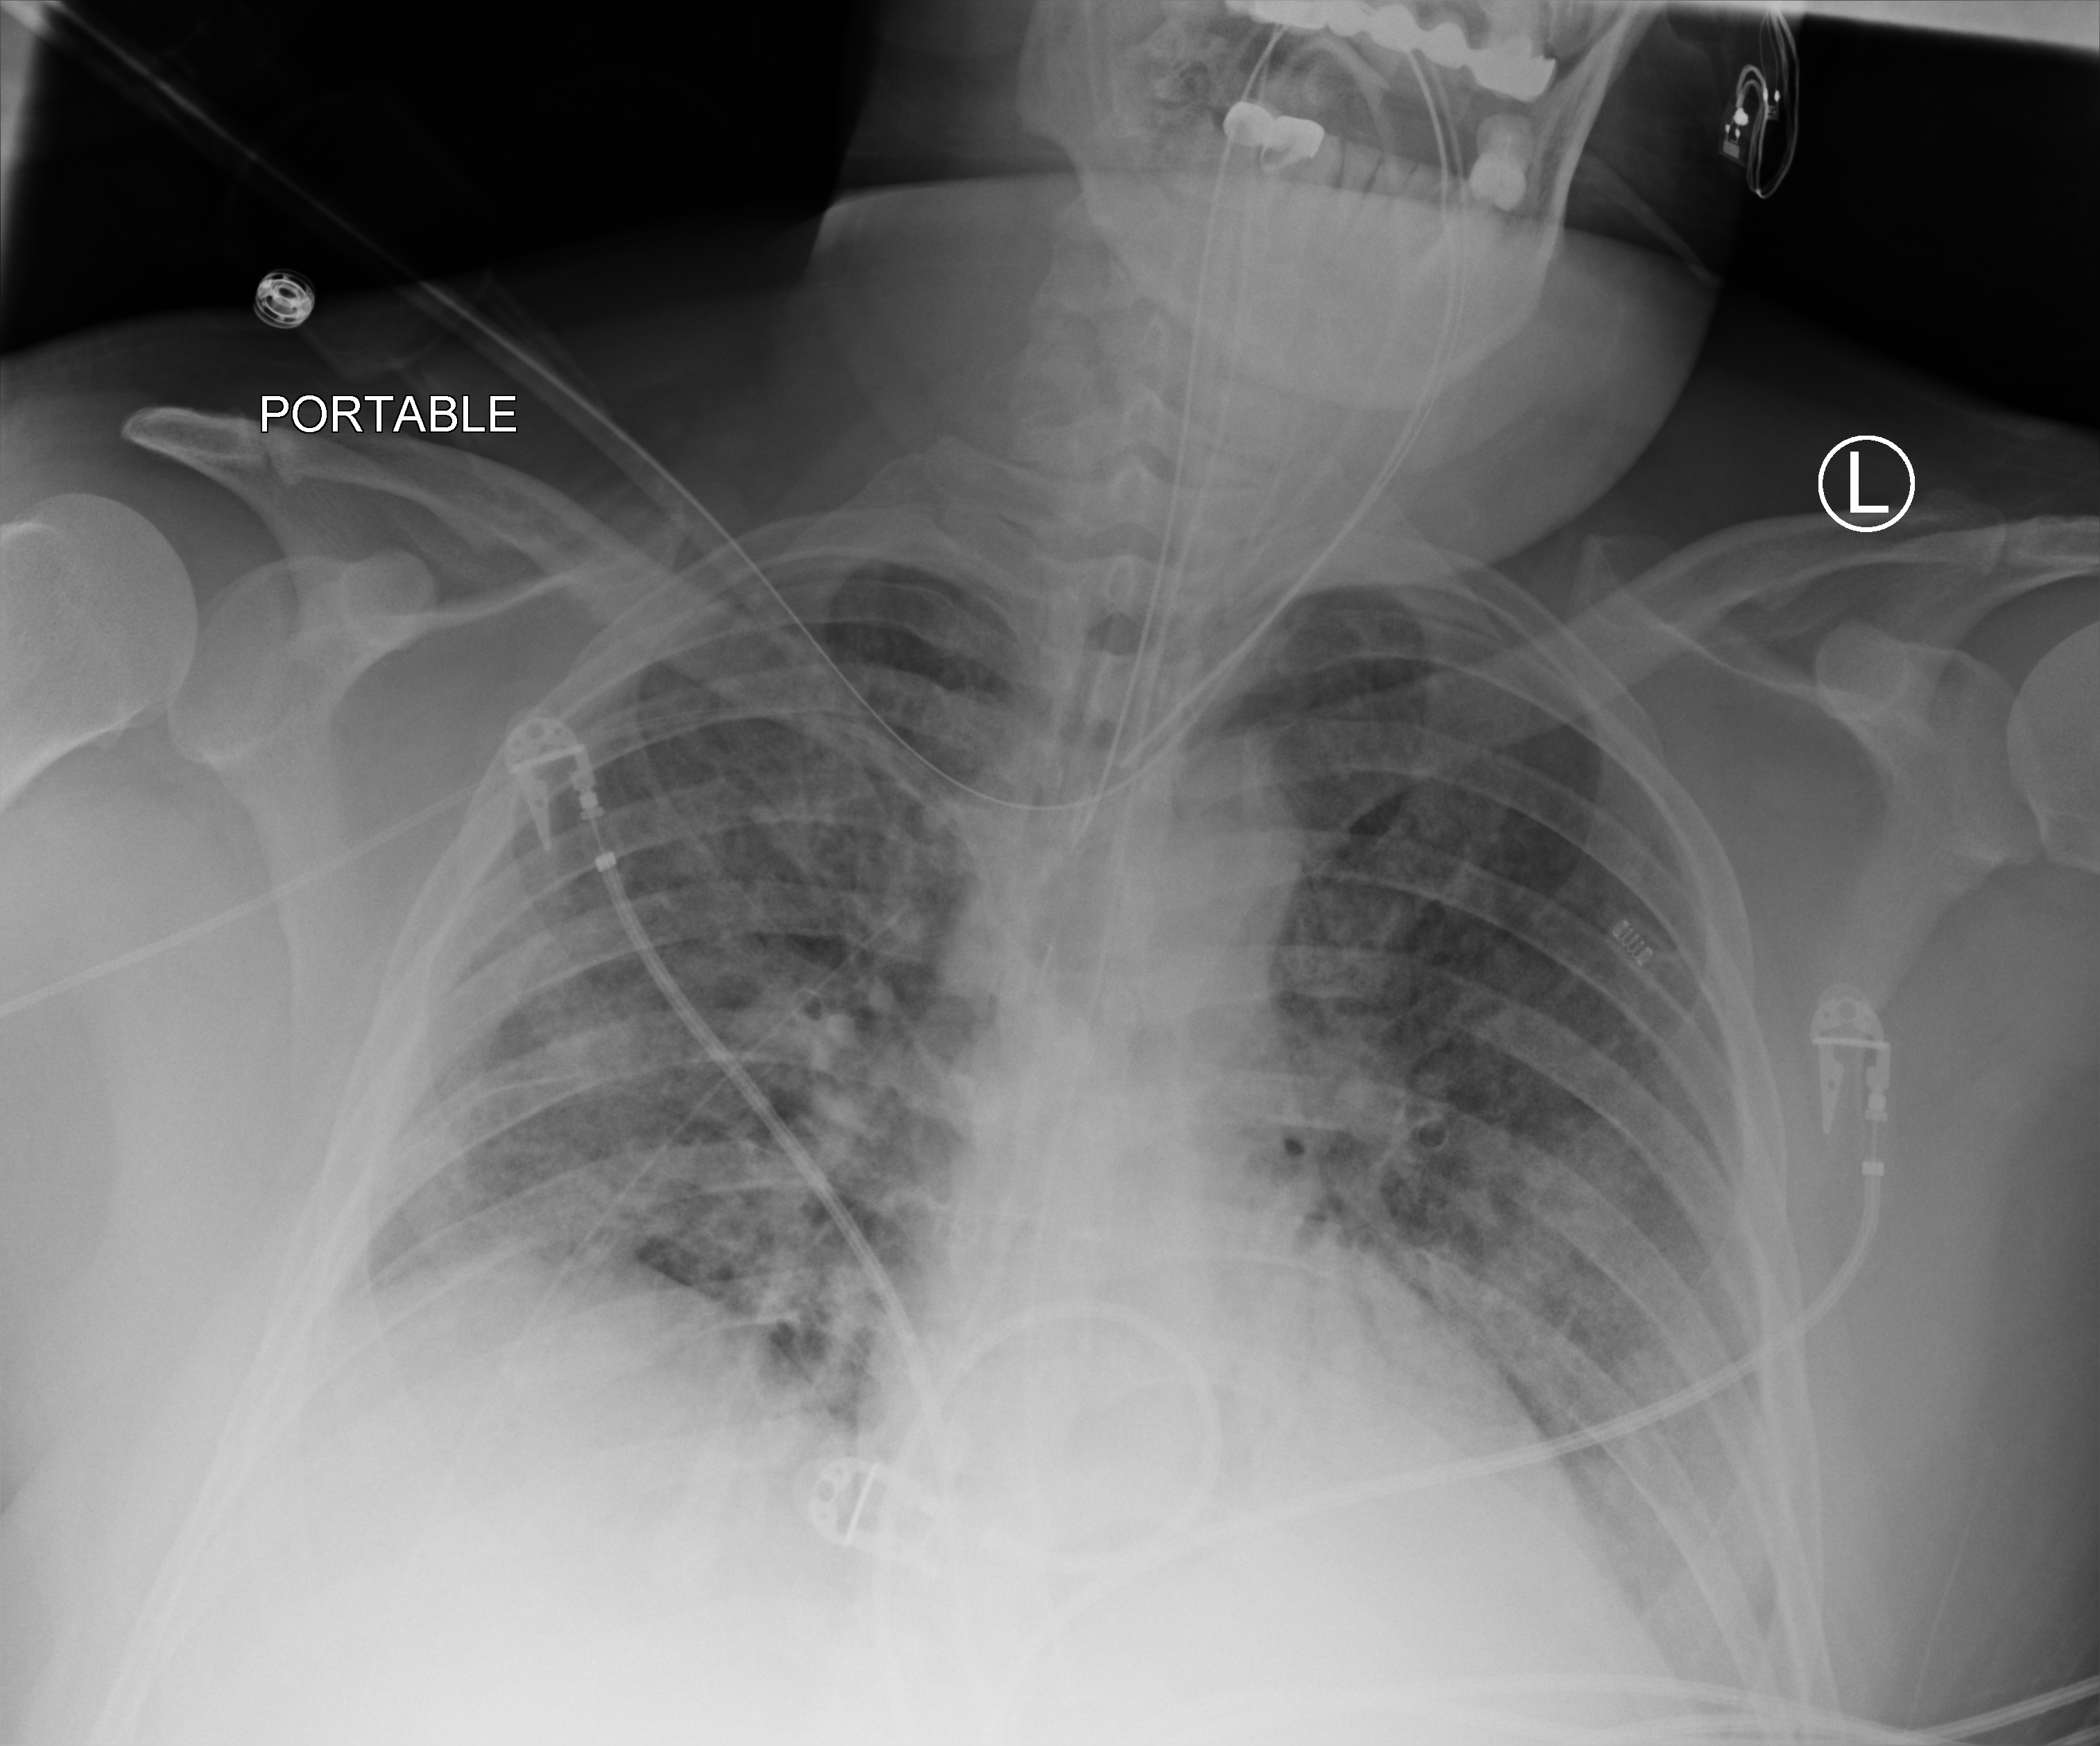
Bedside chest radiograph (computed radiography). Patient hospitalised with COVID-19; male, aged 18–59 years.
Hospital-stay facts (about this admission, not read from this image; timing relative to this image not recorded): admitted to intensive care during this hospital stay: yes.